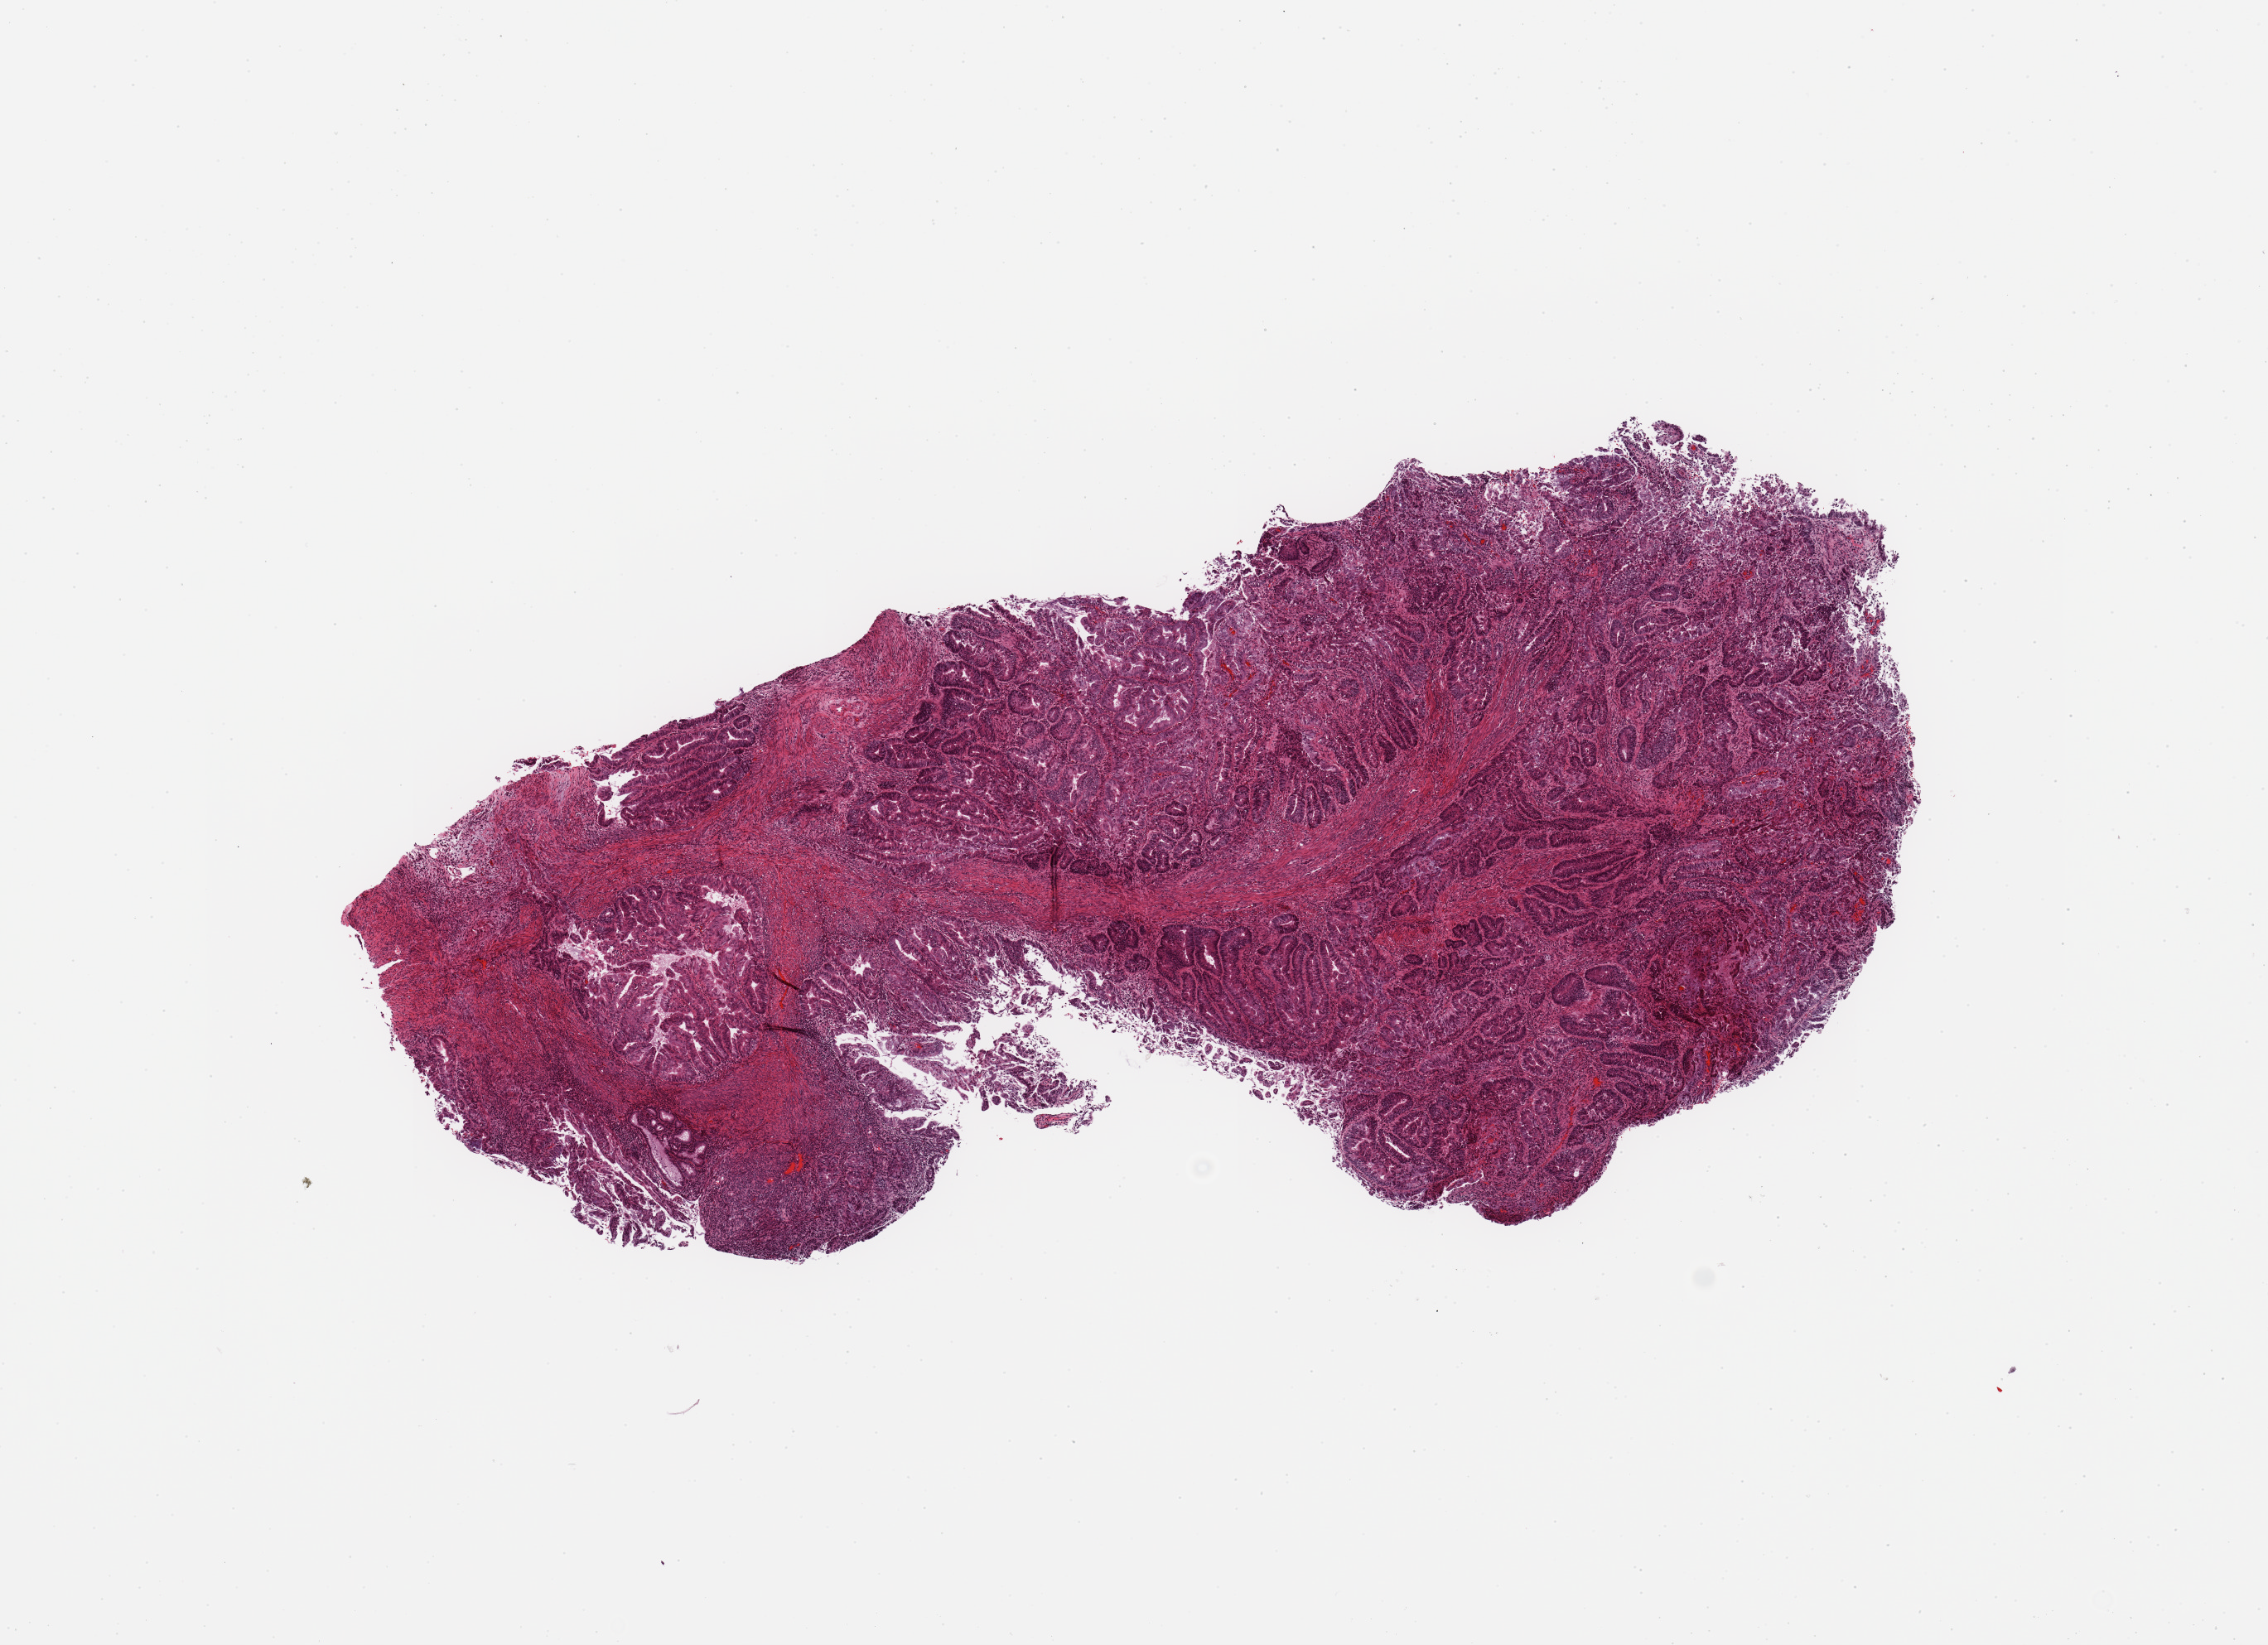
Whole-slide histology image, Hematoxylin and eosin (H&E) stained, shown as a low-resolution overview of the whole scanned area (about 10.8 x 7.9 mm, from a 20x scan). Tumour tissue sample, uterus. 65-year-old female patient. Histologic grade: G2 (moderately differentiated).
• histologic diagnosis: Endometrioid adenocarcinoma, NOS
• AJCC pathologic stage: I